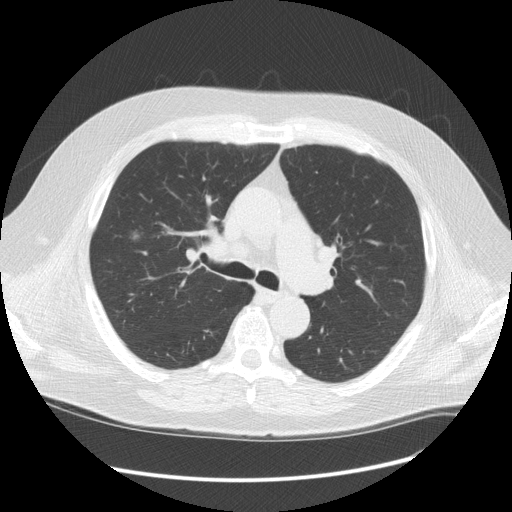
Chest CT (low-dose screening protocol), one axial image; third annual screen; lung window (W 1500 / L -600 HU); standard (soft-tissue) reconstruction kernel (STANDARD); 512 × 512 image matrix, field of view 401 × 401 mm. Male, age 61 years at enrolment. Current smoker at enrolment.
• Lesion marked by an expert reader, box from (x=111, y=216) to (x=153, y=257) px.
• The exam's reader record, not a measurement of the box and not confirmed to be the same lesion: non-calcified nodule or mass ≥4 mm, right upper lobe, 13 × 11 mm, spiculated (stellate) margins, soft tissue attenuation, pre-existing on the prior screen: yes; interval growth: yes.
• Participant outcome: lung cancer diagnosed 21 days after this screen — adenocarcinoma, NOS, right upper lobe, stage IIIA (AJCC 6th edition), 13 mm at pathology.